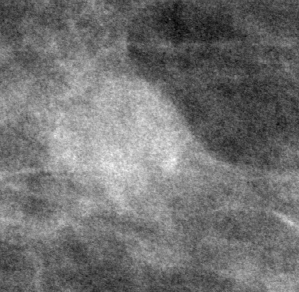
Crop from a digitized film mammogram around one marked abnormality; left breast; MLO view; BI-RADS breast density category 1 (scale 1–4).
Finding: mass, shape lobulated, margins circumscribed; BI-RADS assessment category 3; subtlety rating 5 on a 1 (subtle) to 5 (obvious) scale; pathology (as recorded): benign.